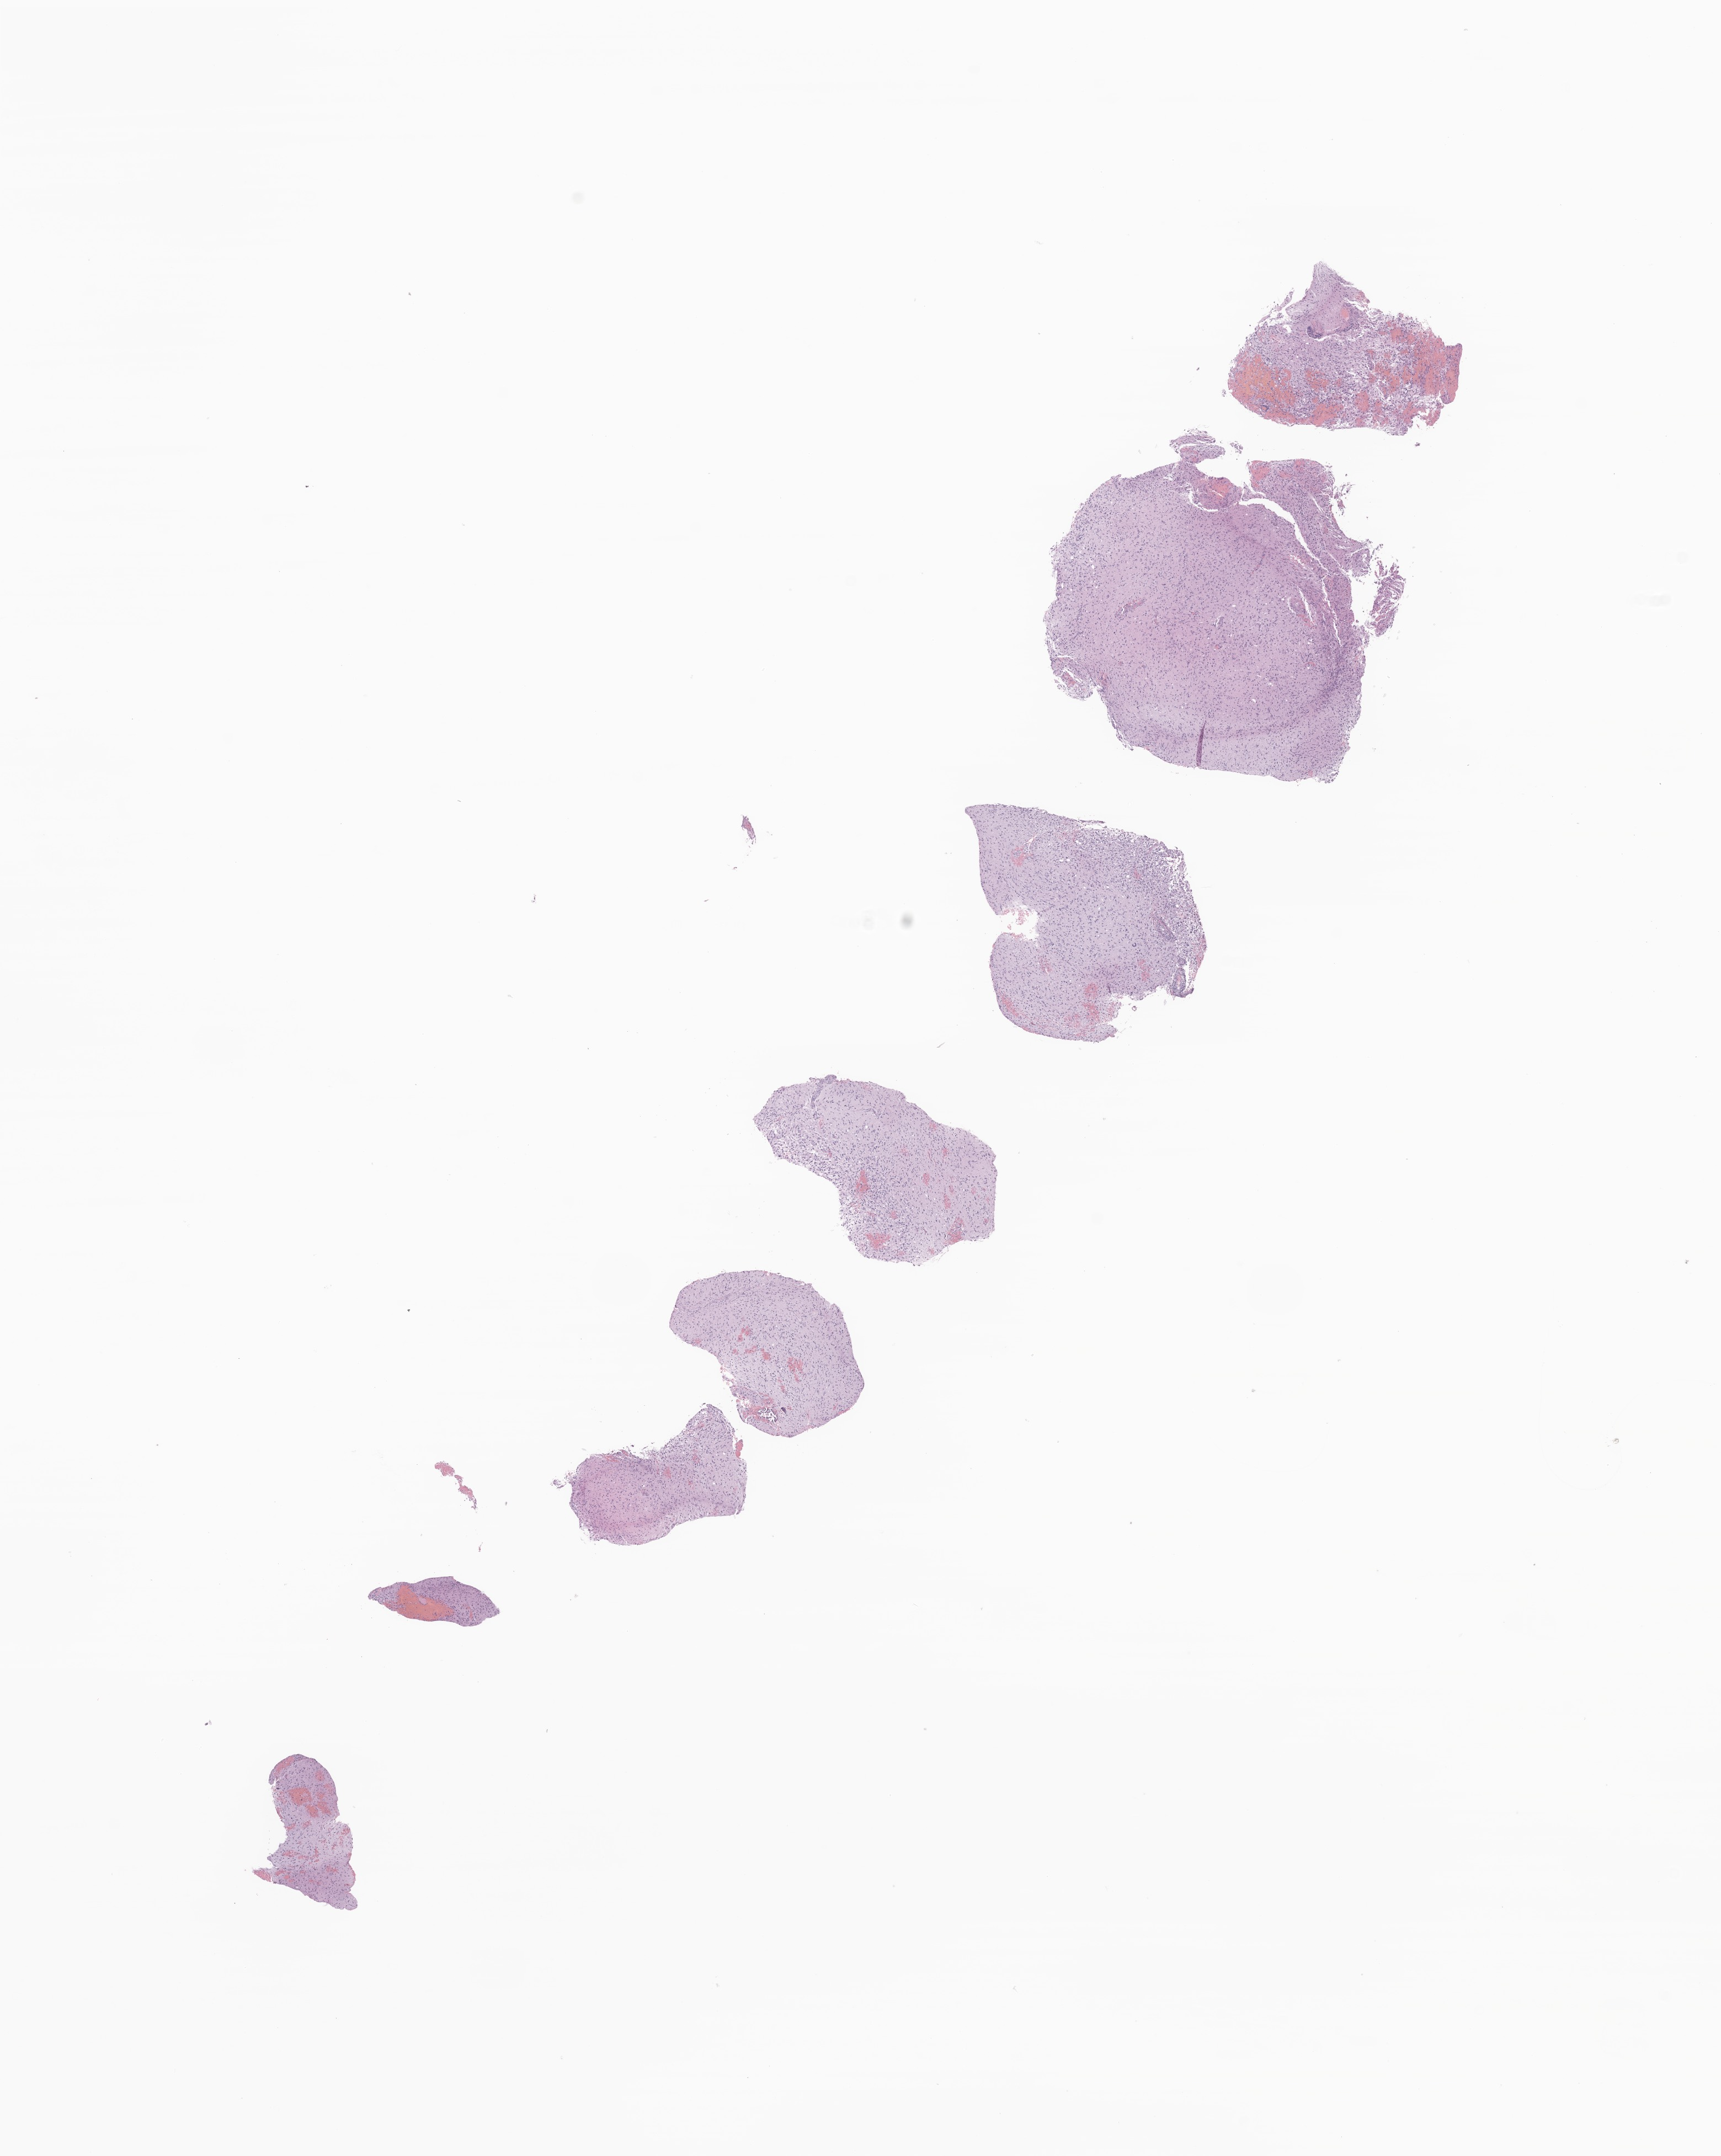
Hematoxylin and eosin (H&E) whole-slide image of tumor tissue from the brain stem — whole scanned area (about 13.1 x 16.5 mm) shown as a low-resolution overview. Formalin-fixed paraffin-embedded section. Male patient, age 100 months.
- diagnosis (ICD-O-3 morphology term): Neoplasm, malignant